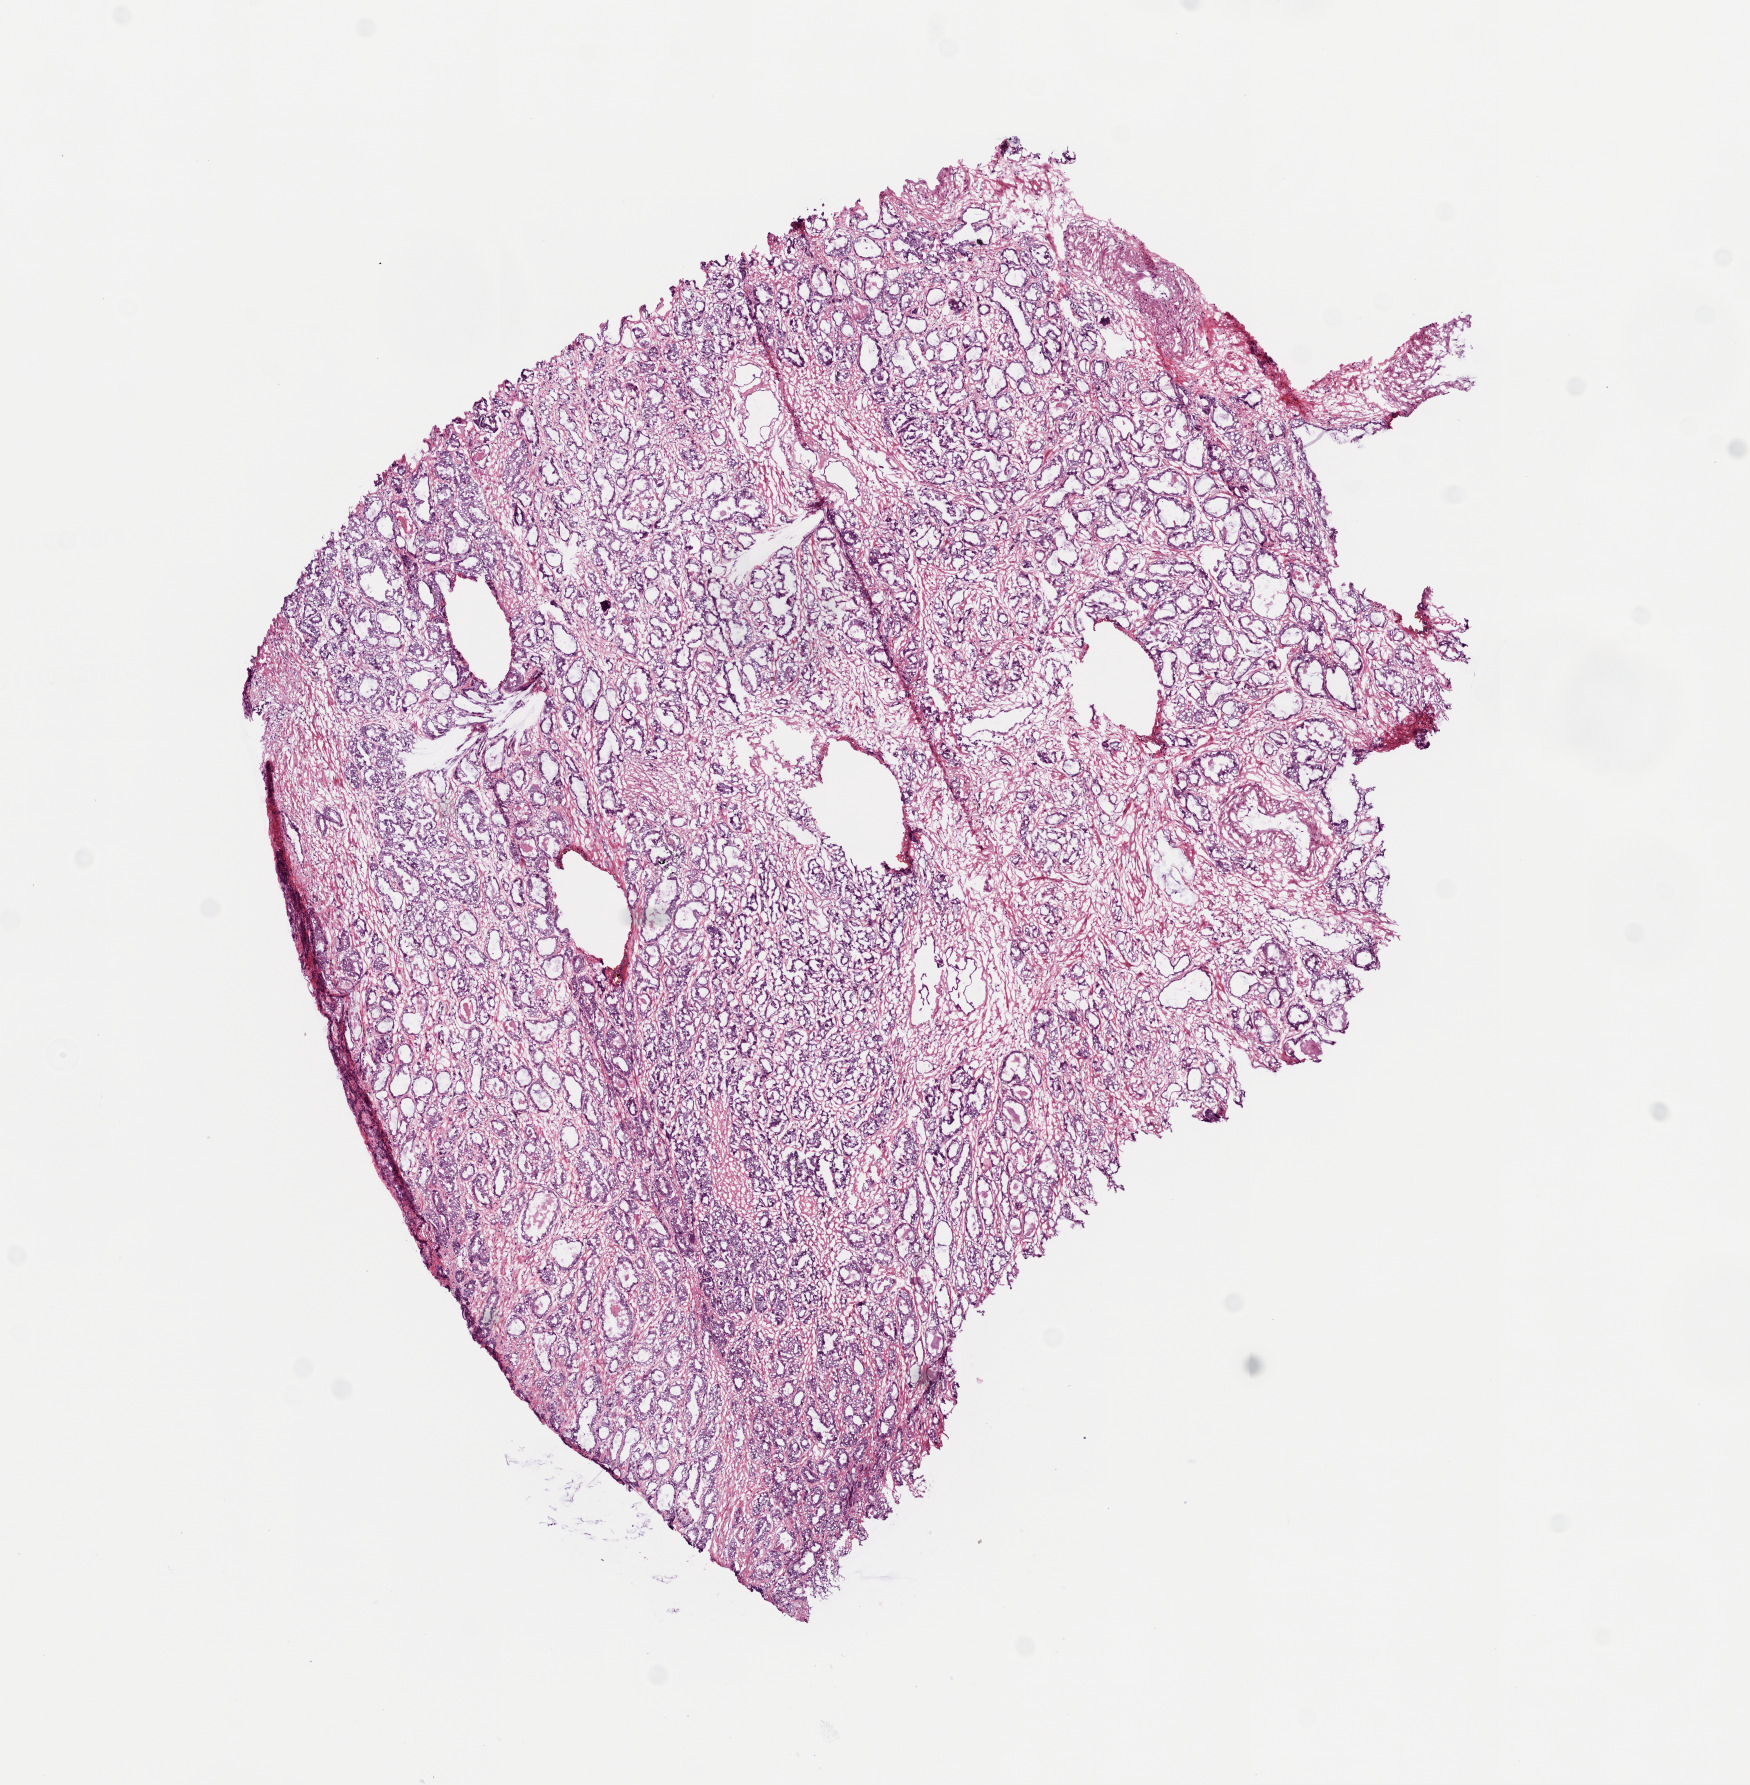
H&E-stained whole-slide image, whole scanned area (about 7.0 x 7.2 mm, acquisition: 20x scan) shown as a low-resolution overview; frozen section from the top of the tissue portion; prostate, primary tumour sample. Male, age 61 years at initial diagnosis. Gleason score: 7 (3+4). Slide review estimates, as recorded: tumour cells 70%, tumour nuclei 70%, normal cells 20%, stromal cells 10%, necrosis 0%.
Laterality: bilateral. Lymph nodes positive (case pathology): 0 of 6 examined. Histologic diagnosis: Acinar cell carcinoma.